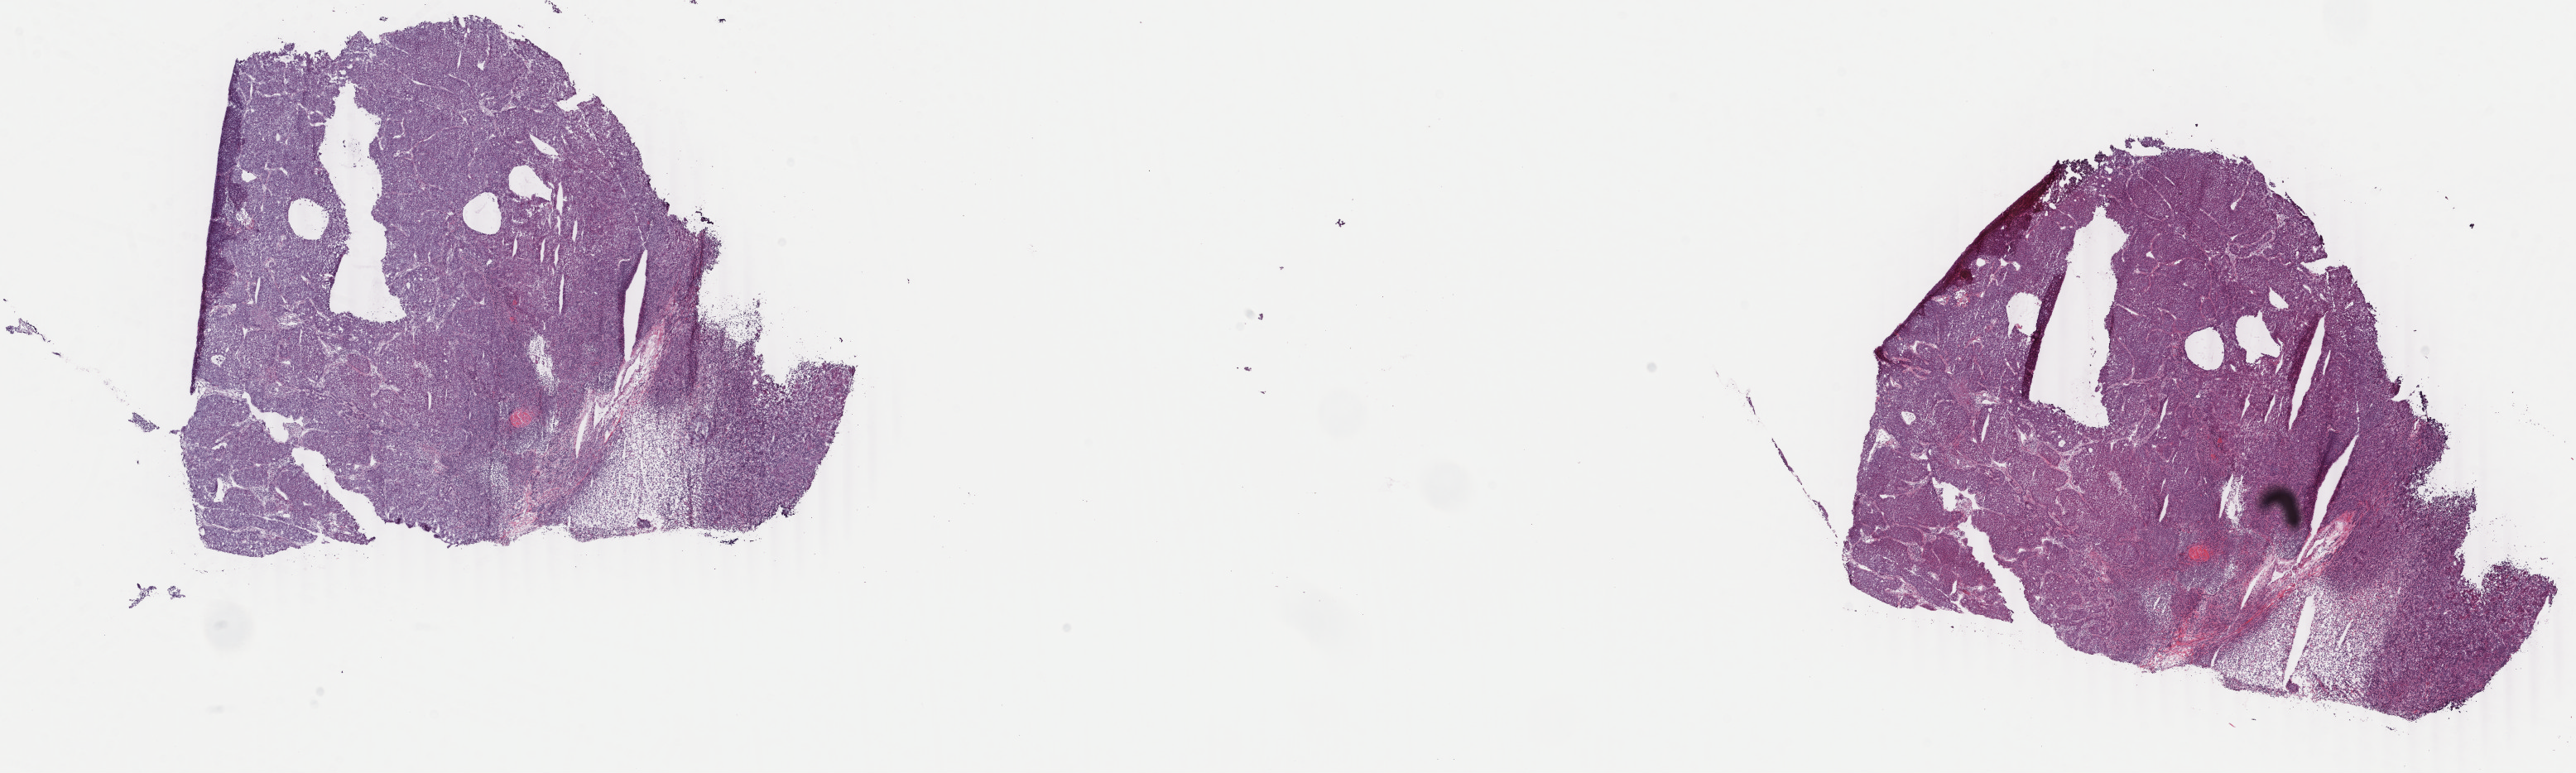
Whole-slide histology image, H&E, low-resolution overview of the scanned area, about 24.7 x 7.4 mm. Frozen section from the top of the tissue portion. Primary tumour sample from the liver. Female patient; age at initial diagnosis 60 years. Histologic grade: G2 (moderately differentiated). Slide review estimates, as recorded: tumour cells 100%, tumour nuclei 80%, normal cells 0%, stromal cells 0%, necrosis 0%. Infiltration values recorded for this section: lymphocyte infiltration 4%, monocyte infiltration 0%, neutrophil infiltration 0%.
Pathologic diagnosis: Hepatocellular carcinoma, NOS. AJCC pathologic stage: II (7th edition).